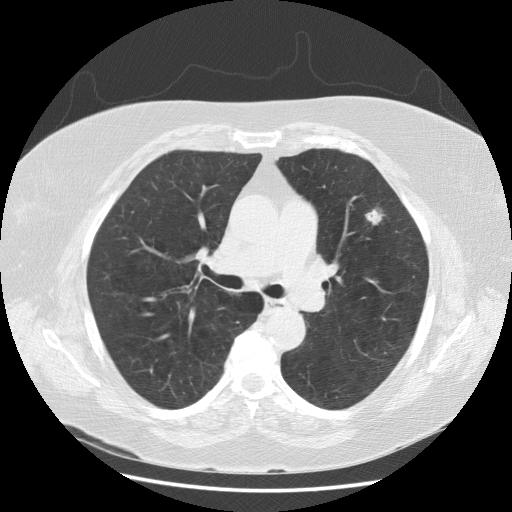
Low-dose screening chest CT, one axial slice. Slice 100 of 164 in the series (ordered by position). Reconstruction kernel STANDARD. 120 kVp. Lung window (W 1500 / L -600 HU). 512 × 512 image matrix.
Annotated regions visible in this slice (manually delineated by an expert):
- lesion 1 (tumor, upper lobe of left lung): box from (x=365, y=209) to (x=385, y=225) px